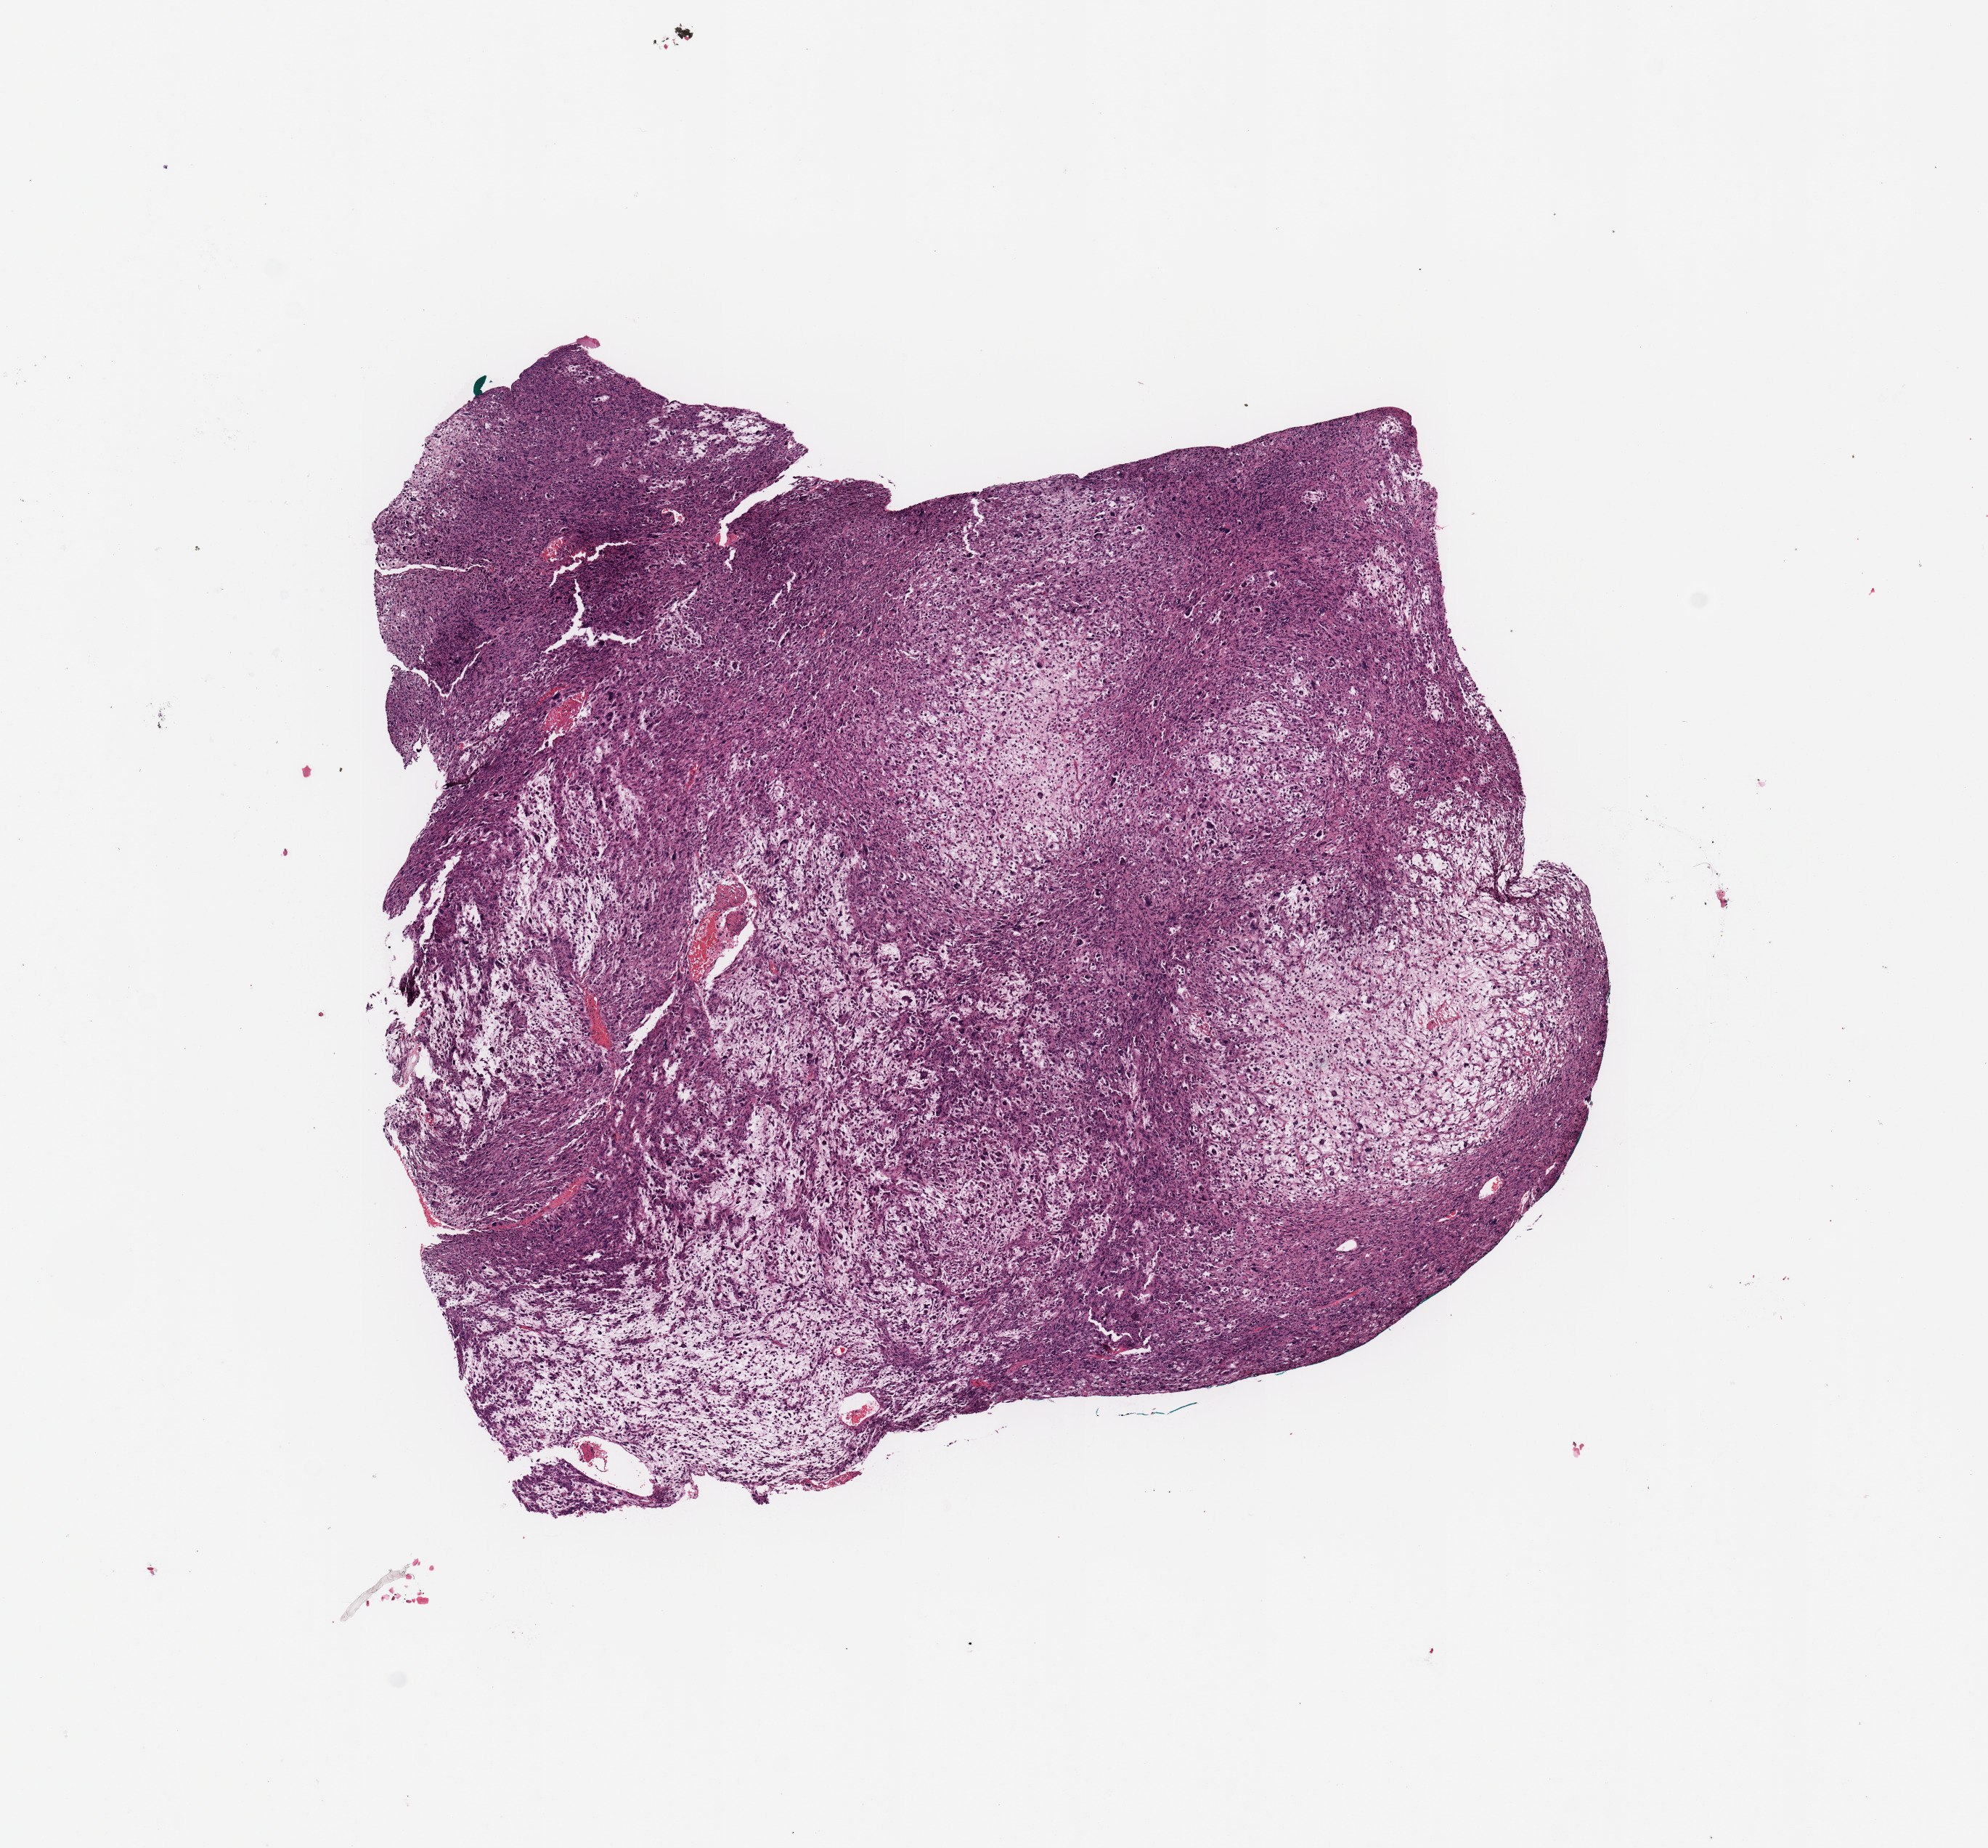
Digitized H&E-stained tissue section (whole slide), low-resolution overview of the scanned area, about 10.8 x 10.1 mm; tumour tissue sample. Female, 62 y/o.
Patient diagnosis (cohort enrolment): sarcoma (site not recorded at cohort level).